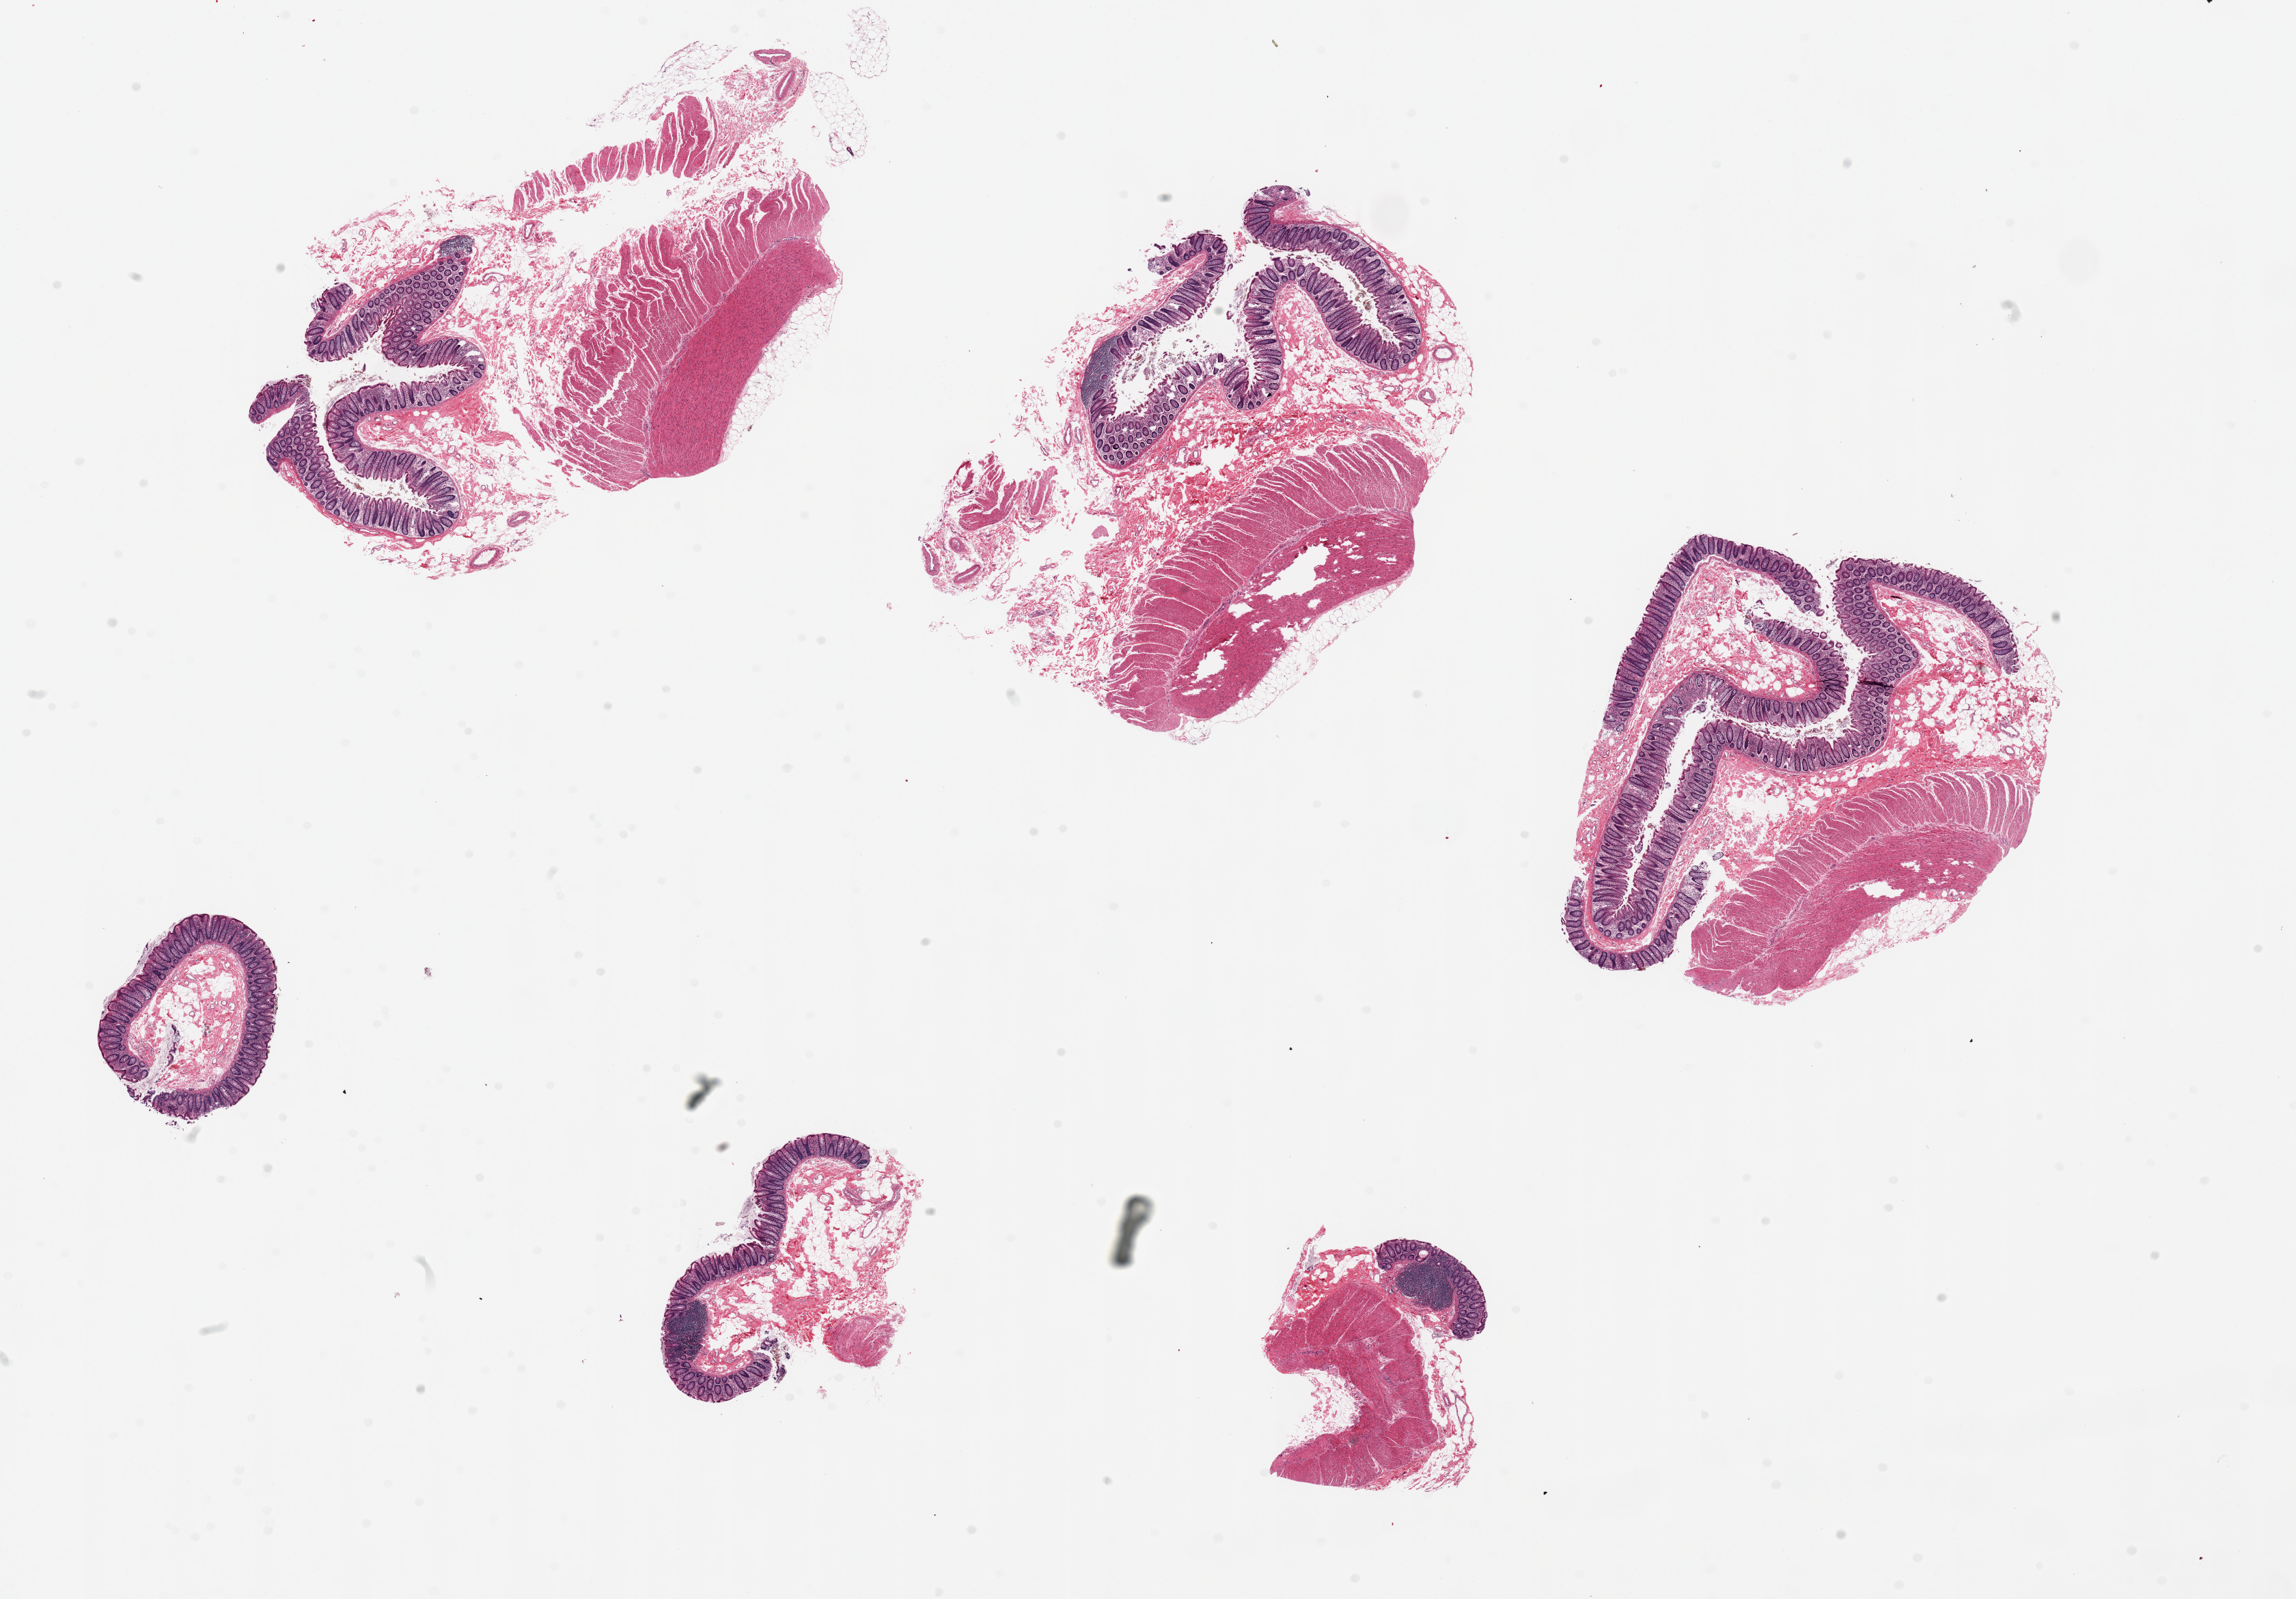
Whole-slide image, H&E stain — a low-resolution overview of the entire scanned area, about 26.6 x 18.5 mm; PAXgene-fixed, paraffin-embedded tissue; target tissue: transverse colon; donor tissue sample. Donor sex: male.
Reviewer comment on this tissue sample: 6 ~5-6mm pieces. Areas of poor fixation. Mucosa is ~ 10% specimen thickness.